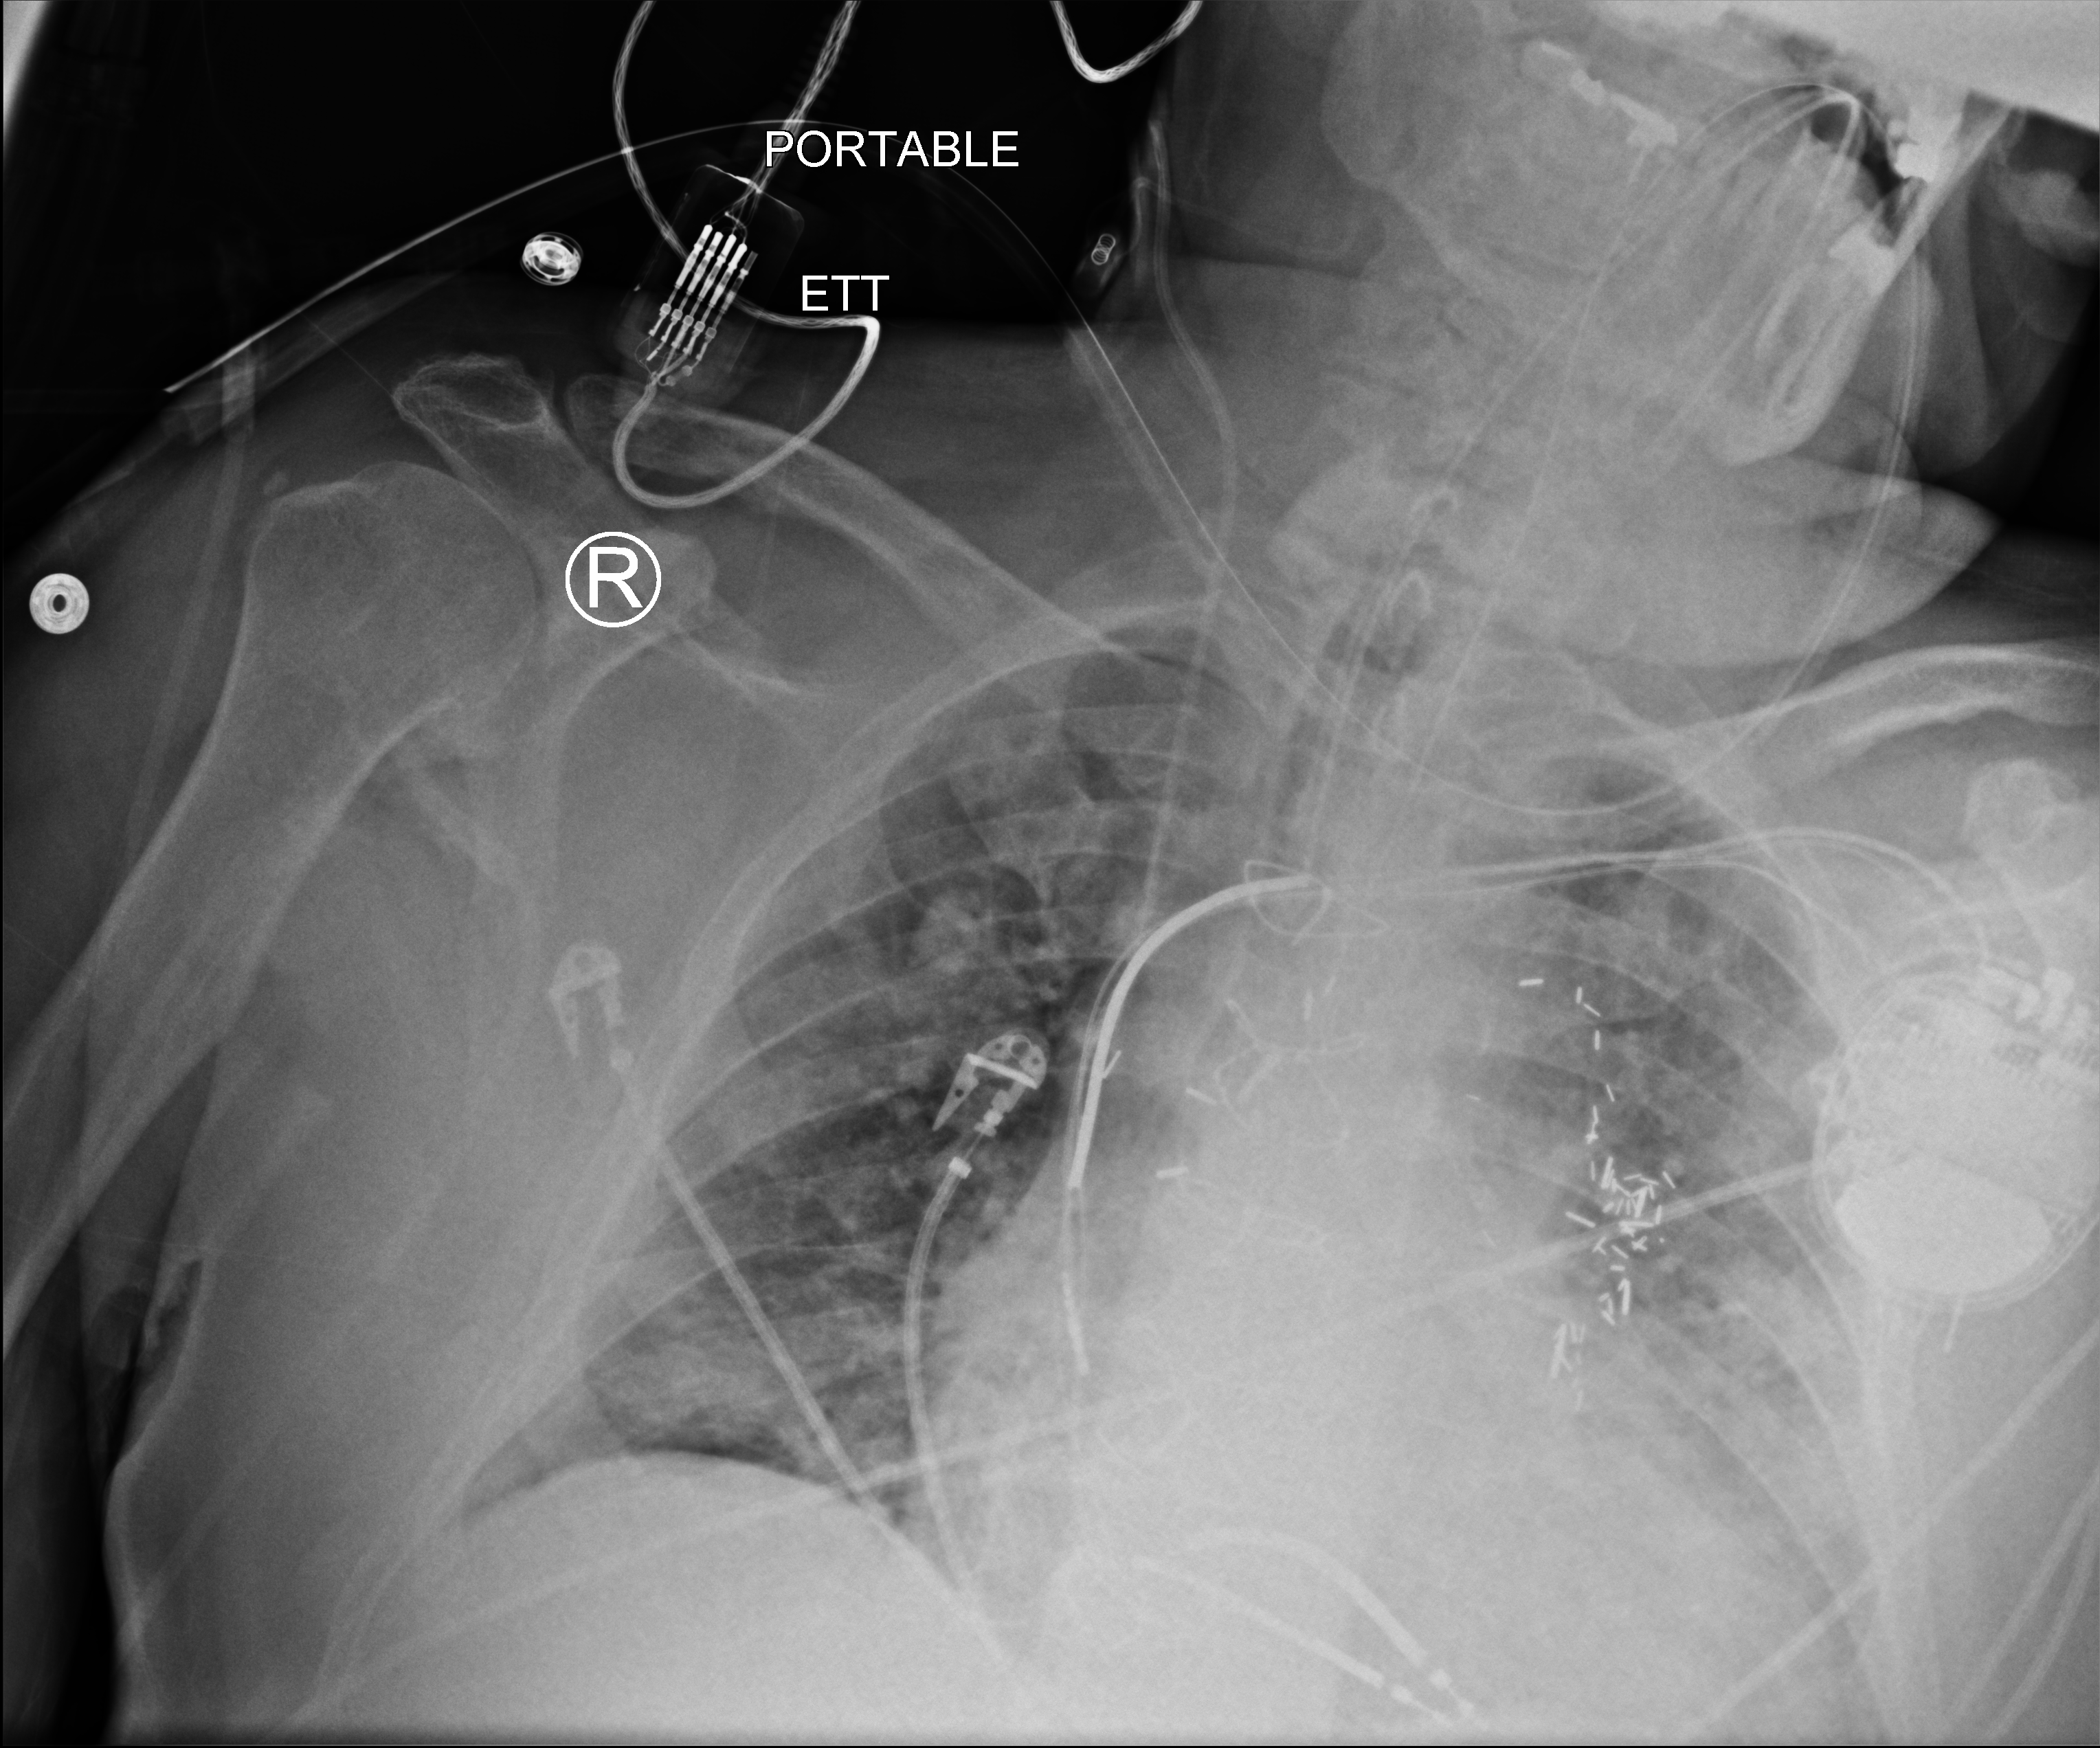
Chest X-ray (portable), anteroposterior (AP) projection. Patient hospitalised with COVID-19; male, aged 60–74 years.
Hospital-stay facts (about this admission, not read from this image; timing relative to this image not recorded):
- diabetes (admission record): yes
- chronic kidney disease (admission record): no
- admitted to intensive care during this hospital stay: yes